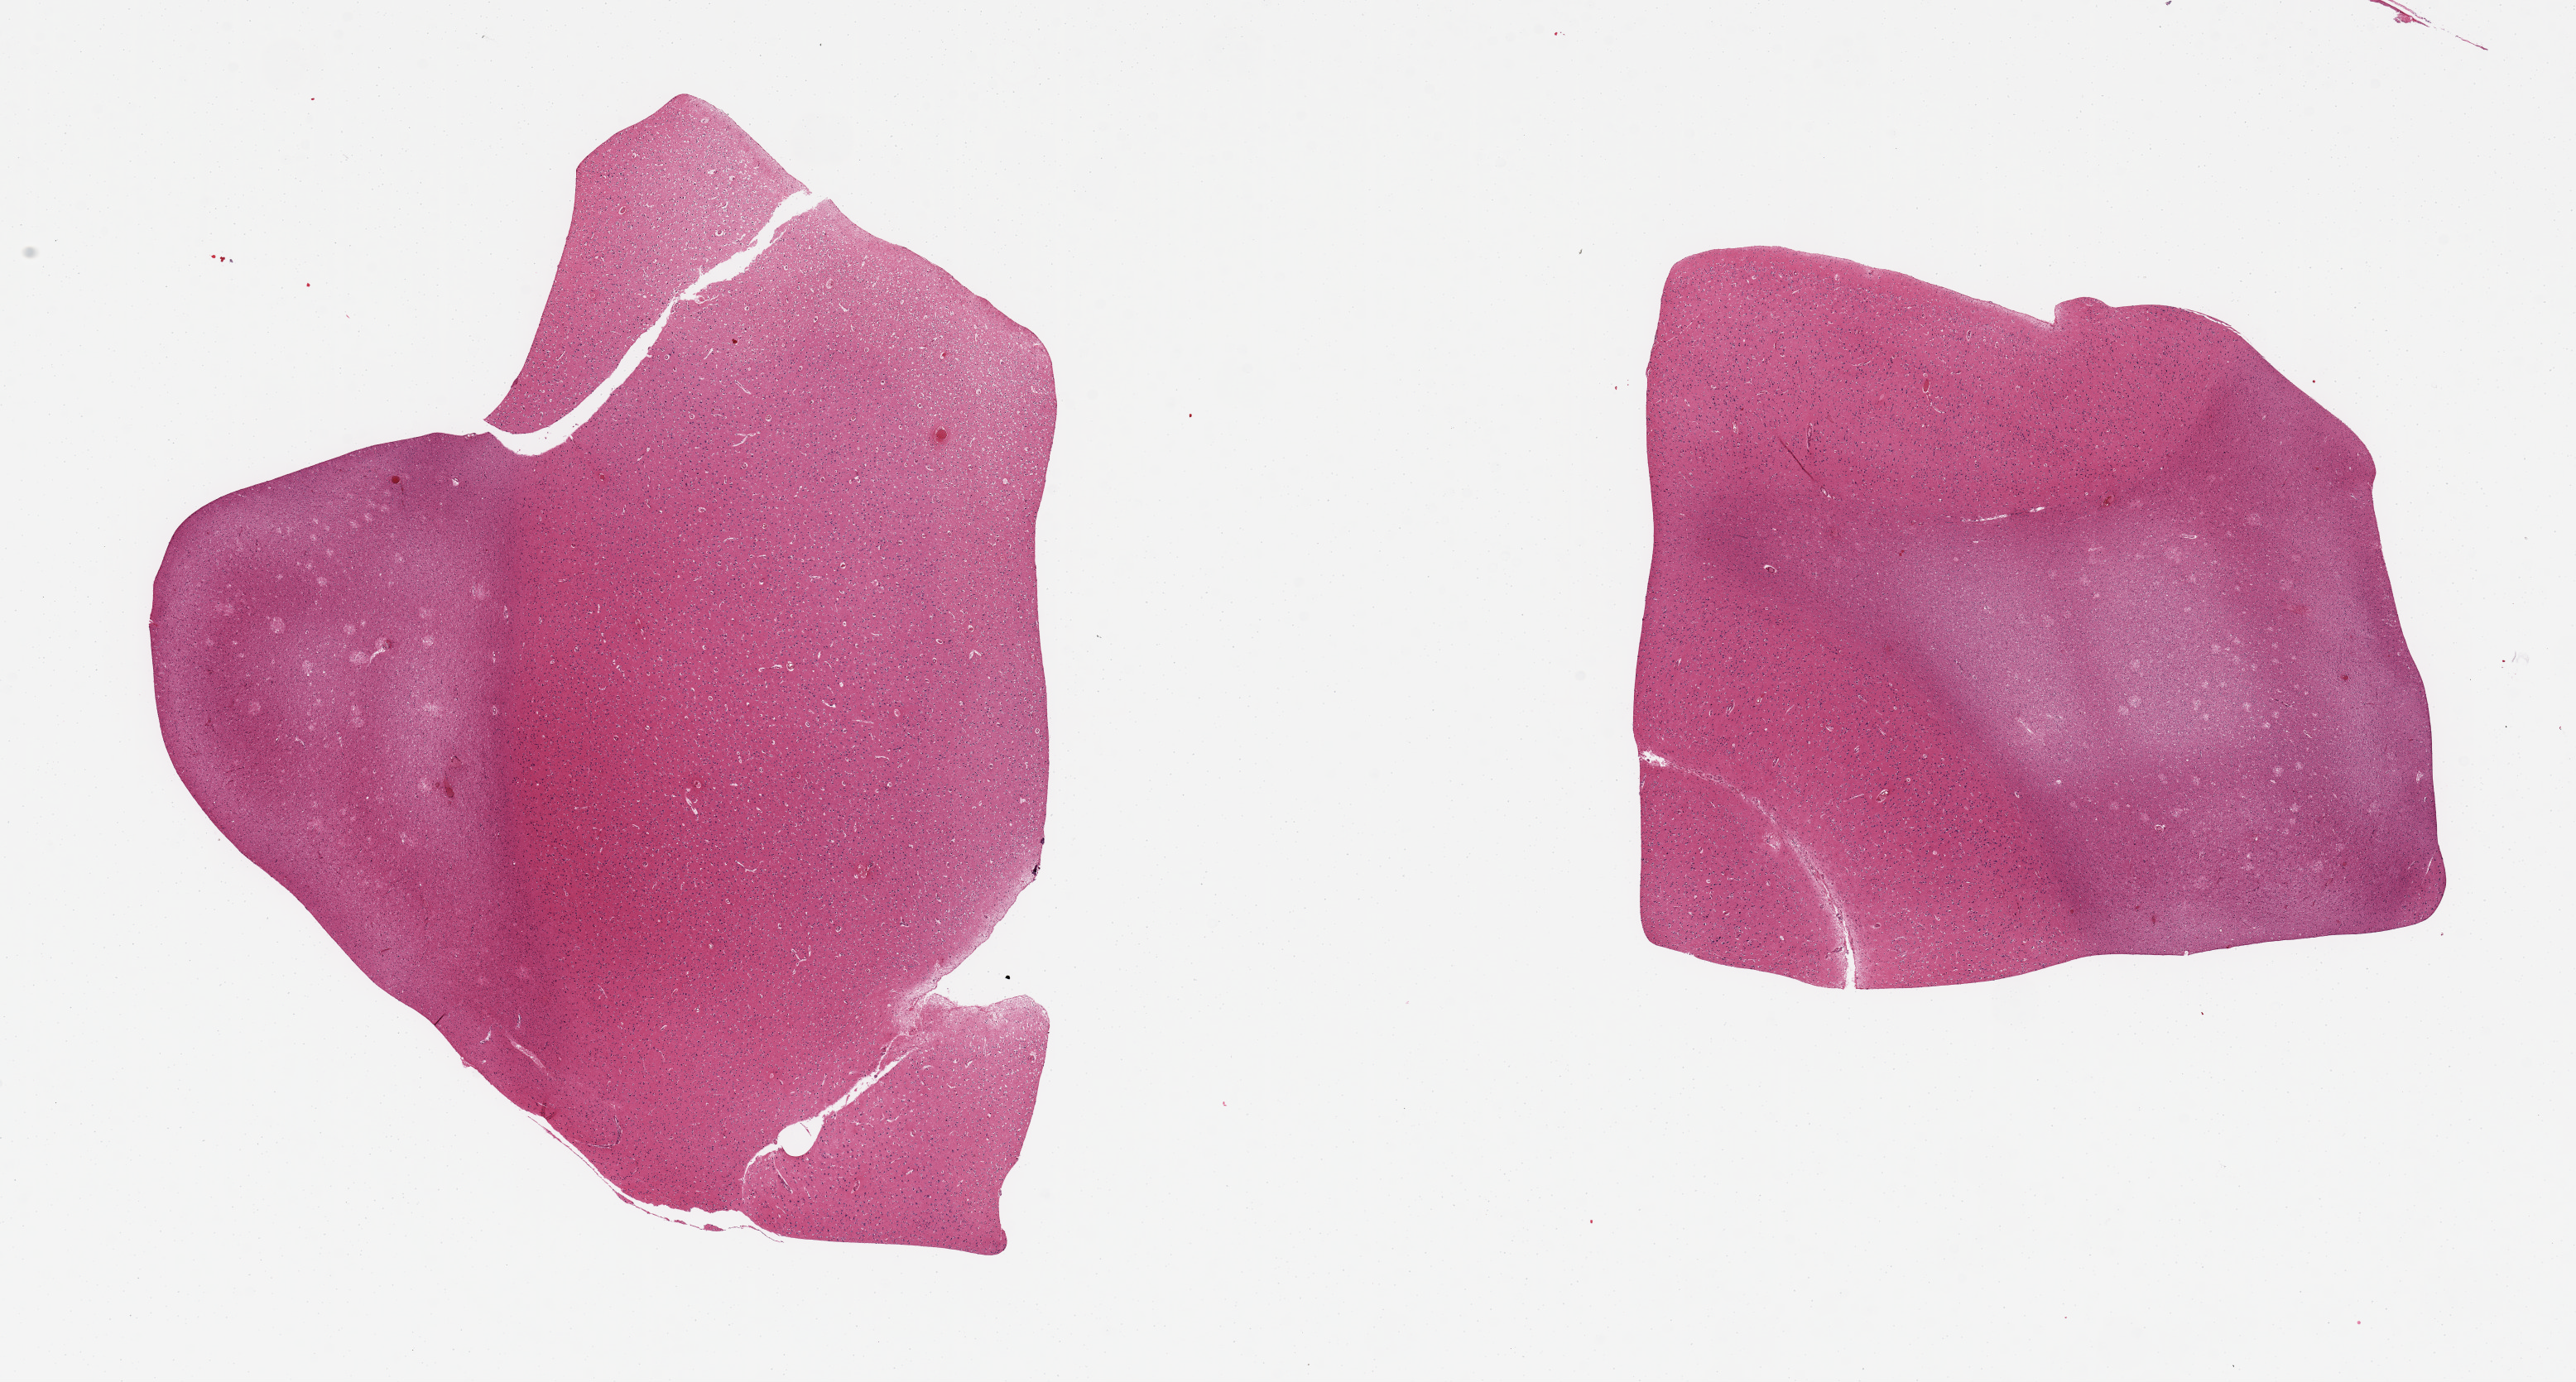
Digitized haematoxylin and eosin-stained section — a low-resolution overview of the entire scanned area, about 24.6 x 13.2 mm (slide scanned at 20x). PAXgene-fixed, paraffin-embedded tissue. Sampled site (target tissue): cerebral cortex. Donor tissue sample. Donor: male.
Pathologist's review note for this sample: 2 pieces.